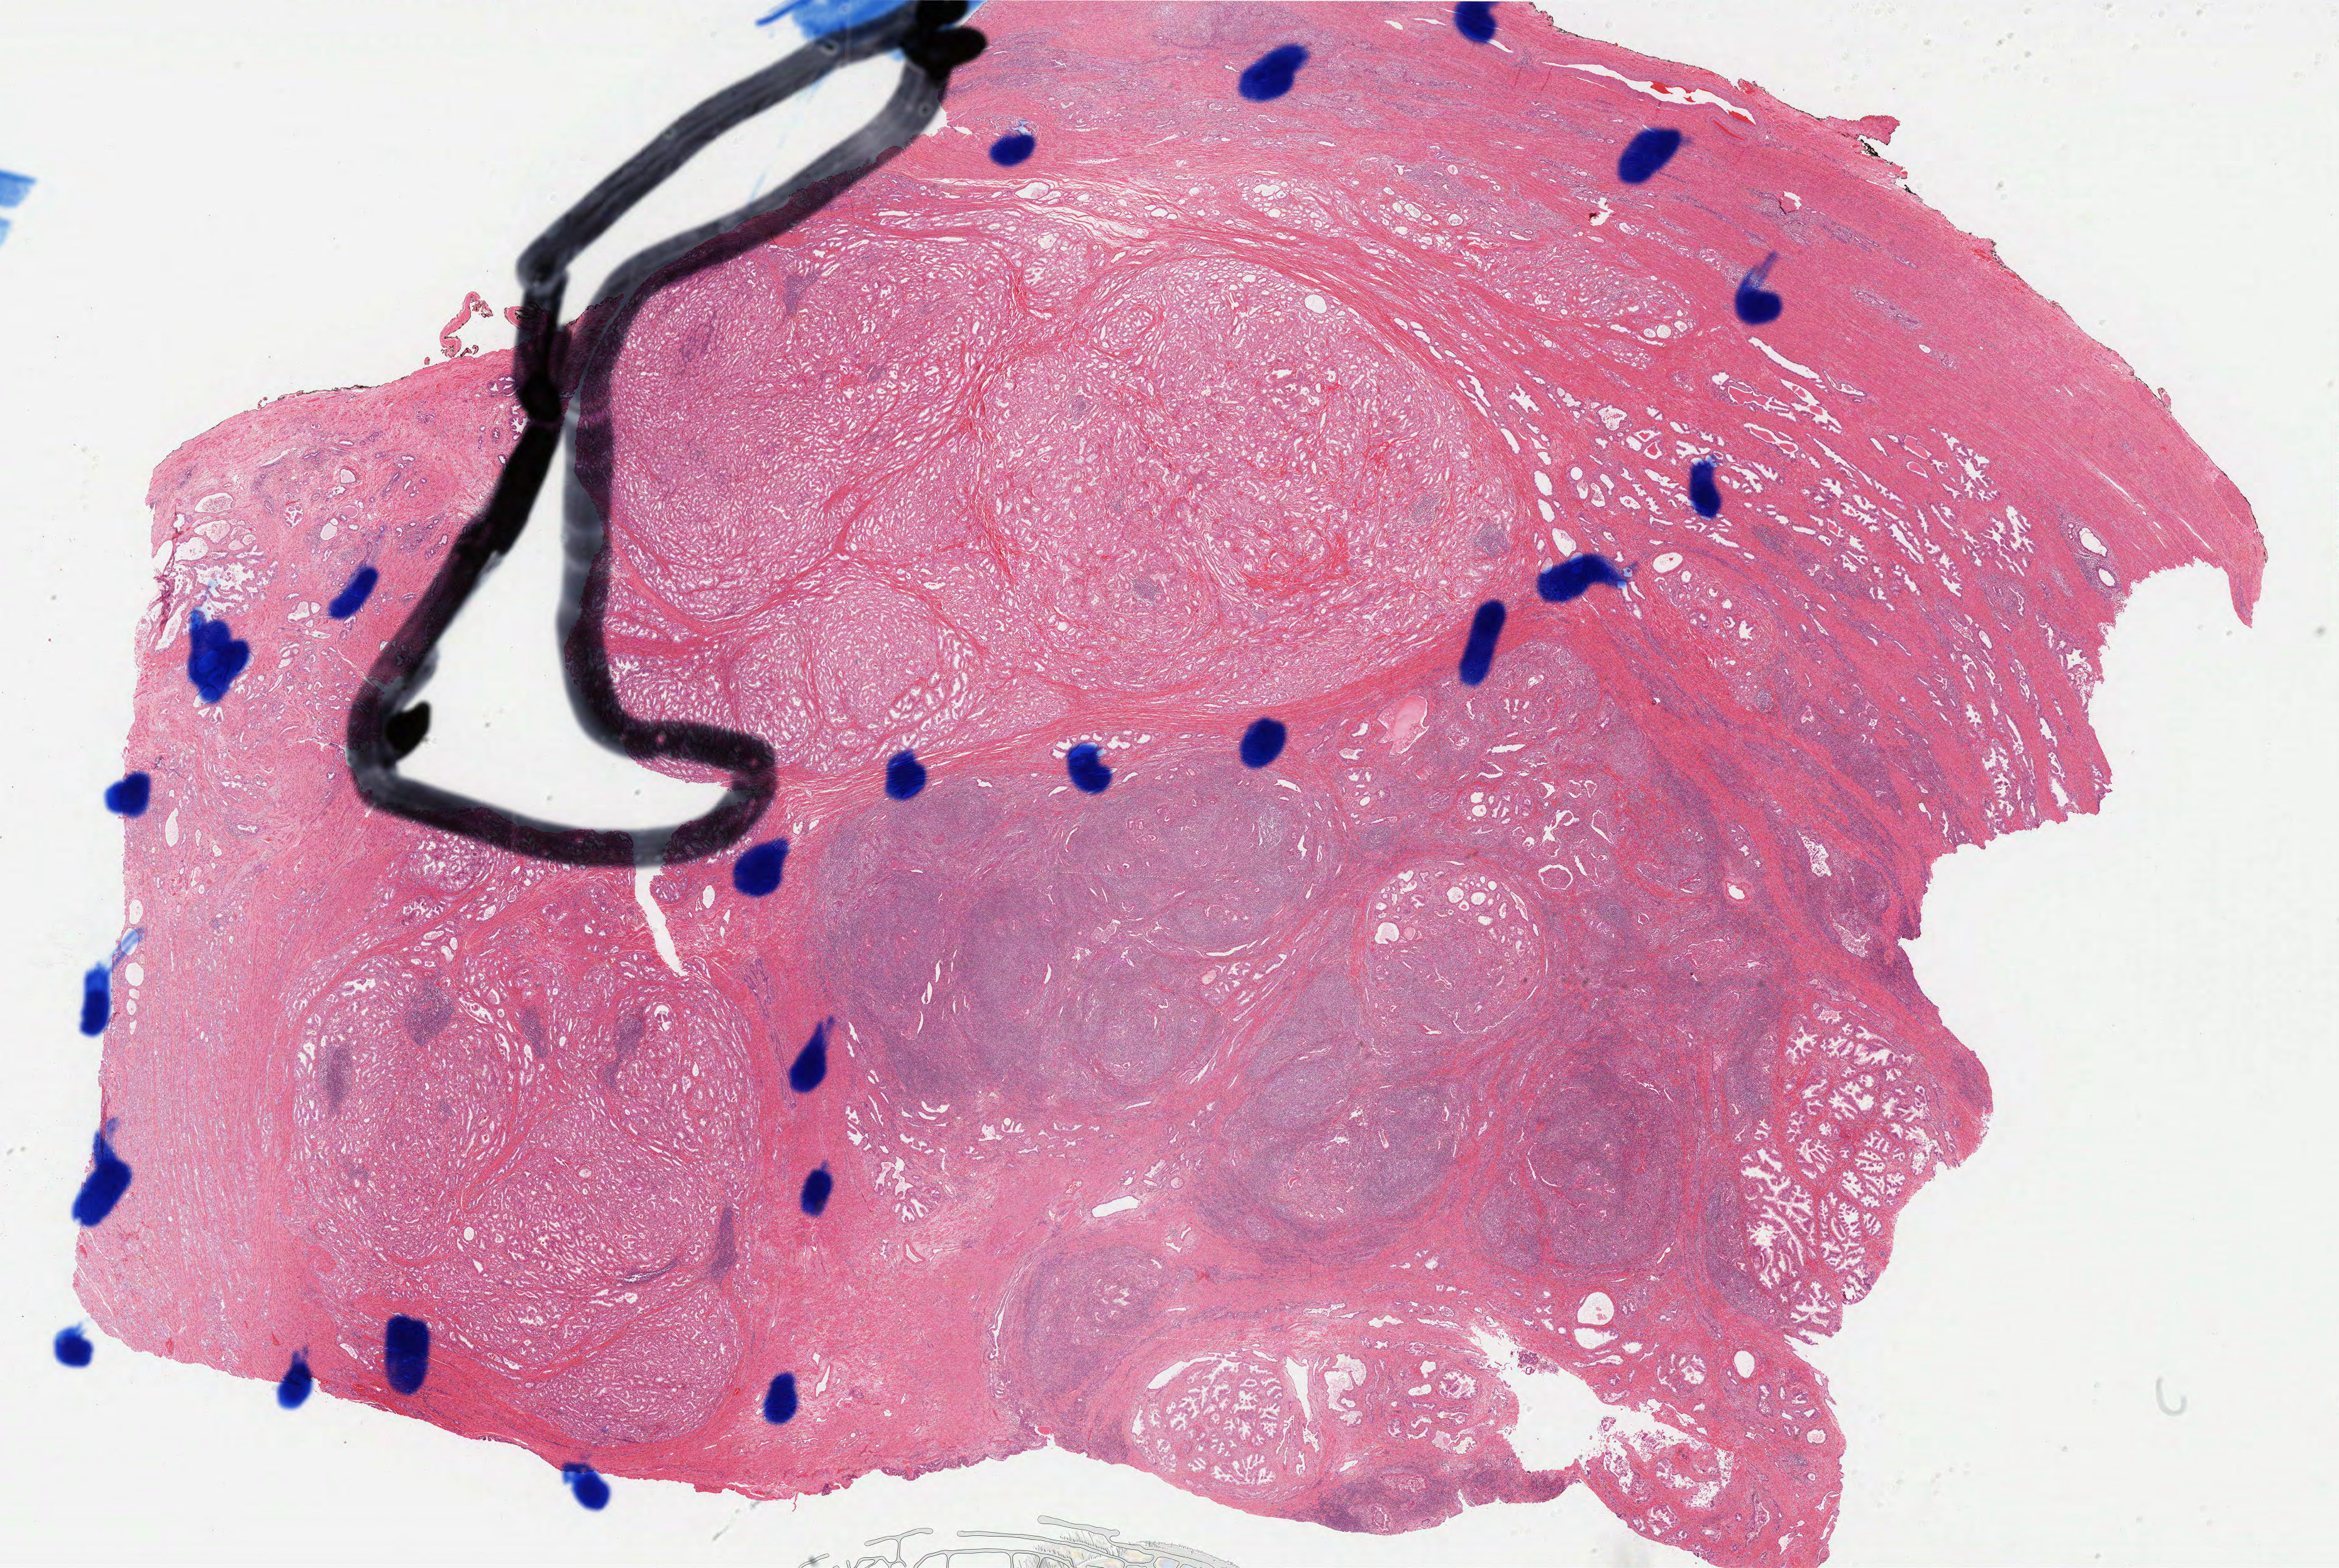
Digitized H&E tissue section (whole slide), a low-resolution overview of the entire scanned area, about 29.8 x 20.0 mm (from a 40x scan), formalin-fixed paraffin-embedded (FFPE) diagnostic section, primary tumour sample from the prostate. Patient: male, age at initial diagnosis 59 years. Gleason score: 6 (3+3).
Pathologic diagnosis: Adenocarcinoma, NOS (prostate gland). Lymph nodes positive (case pathology): 0 of 12 examined.